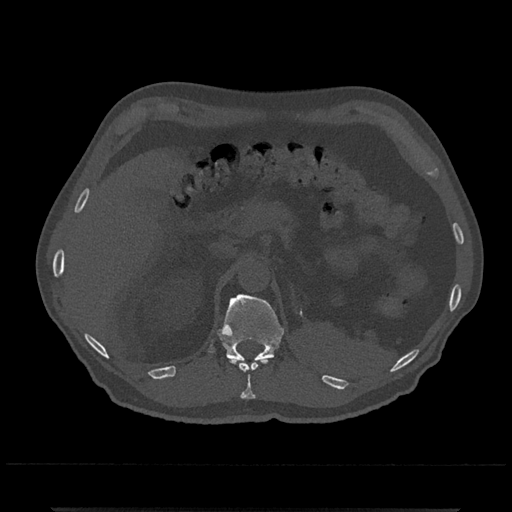
CT including the spine, one axial slice. Position 451 of 797 along the scan axis. Reconstruction kernel Br40s/3. Bone window (W 1800 / L 400 HU). 0.5 mm slice thickness. 512 × 512 image matrix, field of view 393 × 393 mm. Male patient, age 67 years. From the clinical record (not read from this slice): primary cancer: prostate.
Outlined on this slice (semi-automatically segmented with operator editing):
- T11 vertebra: bounding box [x1, y1, x2, y2] px = [229, 358, 267, 399]
- T12 vertebra: [217, 294, 284, 363]